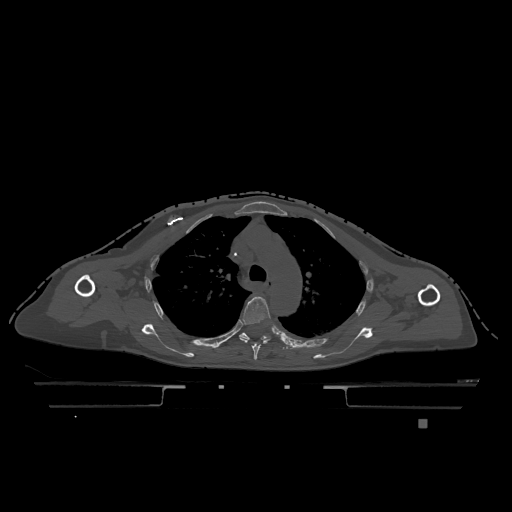
CT including the spine, one axial slice. Bone window (W 1800 / L 400 HU). 0.5 mm slice thickness. 512 × 512 image matrix. Patient: female, 74 years. Case-level facts recorded for this patient, not image findings: primary cancer: lung; vertebrae with lytic lesions (as recorded): T1, T4, T5, T6, L4, L5.
Structures marked on this image (semi-automatically segmented with operator editing):
- T4 vertebra: box from (x=239, y=296) to (x=272, y=360) px
- T5 vertebra: (x=239, y=332)–(x=285, y=349)